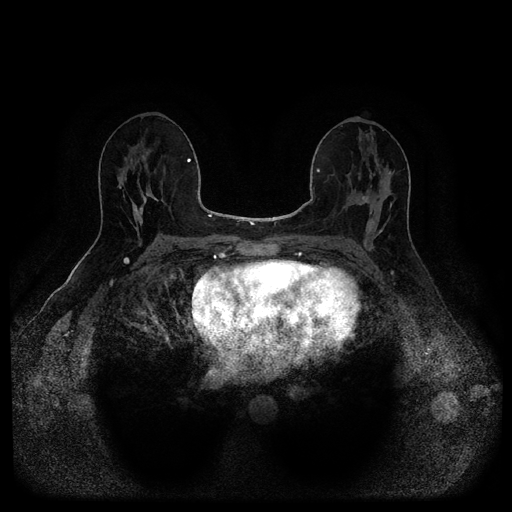
Breast MRI (dynamic contrast-enhanced, multi-phase), one axial slice. Slice 58 of 116 in the series (ordered by position). Dynamic contrast-enhanced series, time point 2 of 5 at this slice position (early post-contrast). 1.5 T. TE 2.6 ms, TR 5.3 ms. 2.2 mm slice thickness. 512 × 512 image matrix, field of view 350 × 350 mm. Patient: female, 49 years.
Outlined on this slice (semi-automatically segmented with operator editing):
- breast lesion (labelled benign in the annotation): bounding box [x1, y1, x2, y2] px = [365, 217, 377, 234]